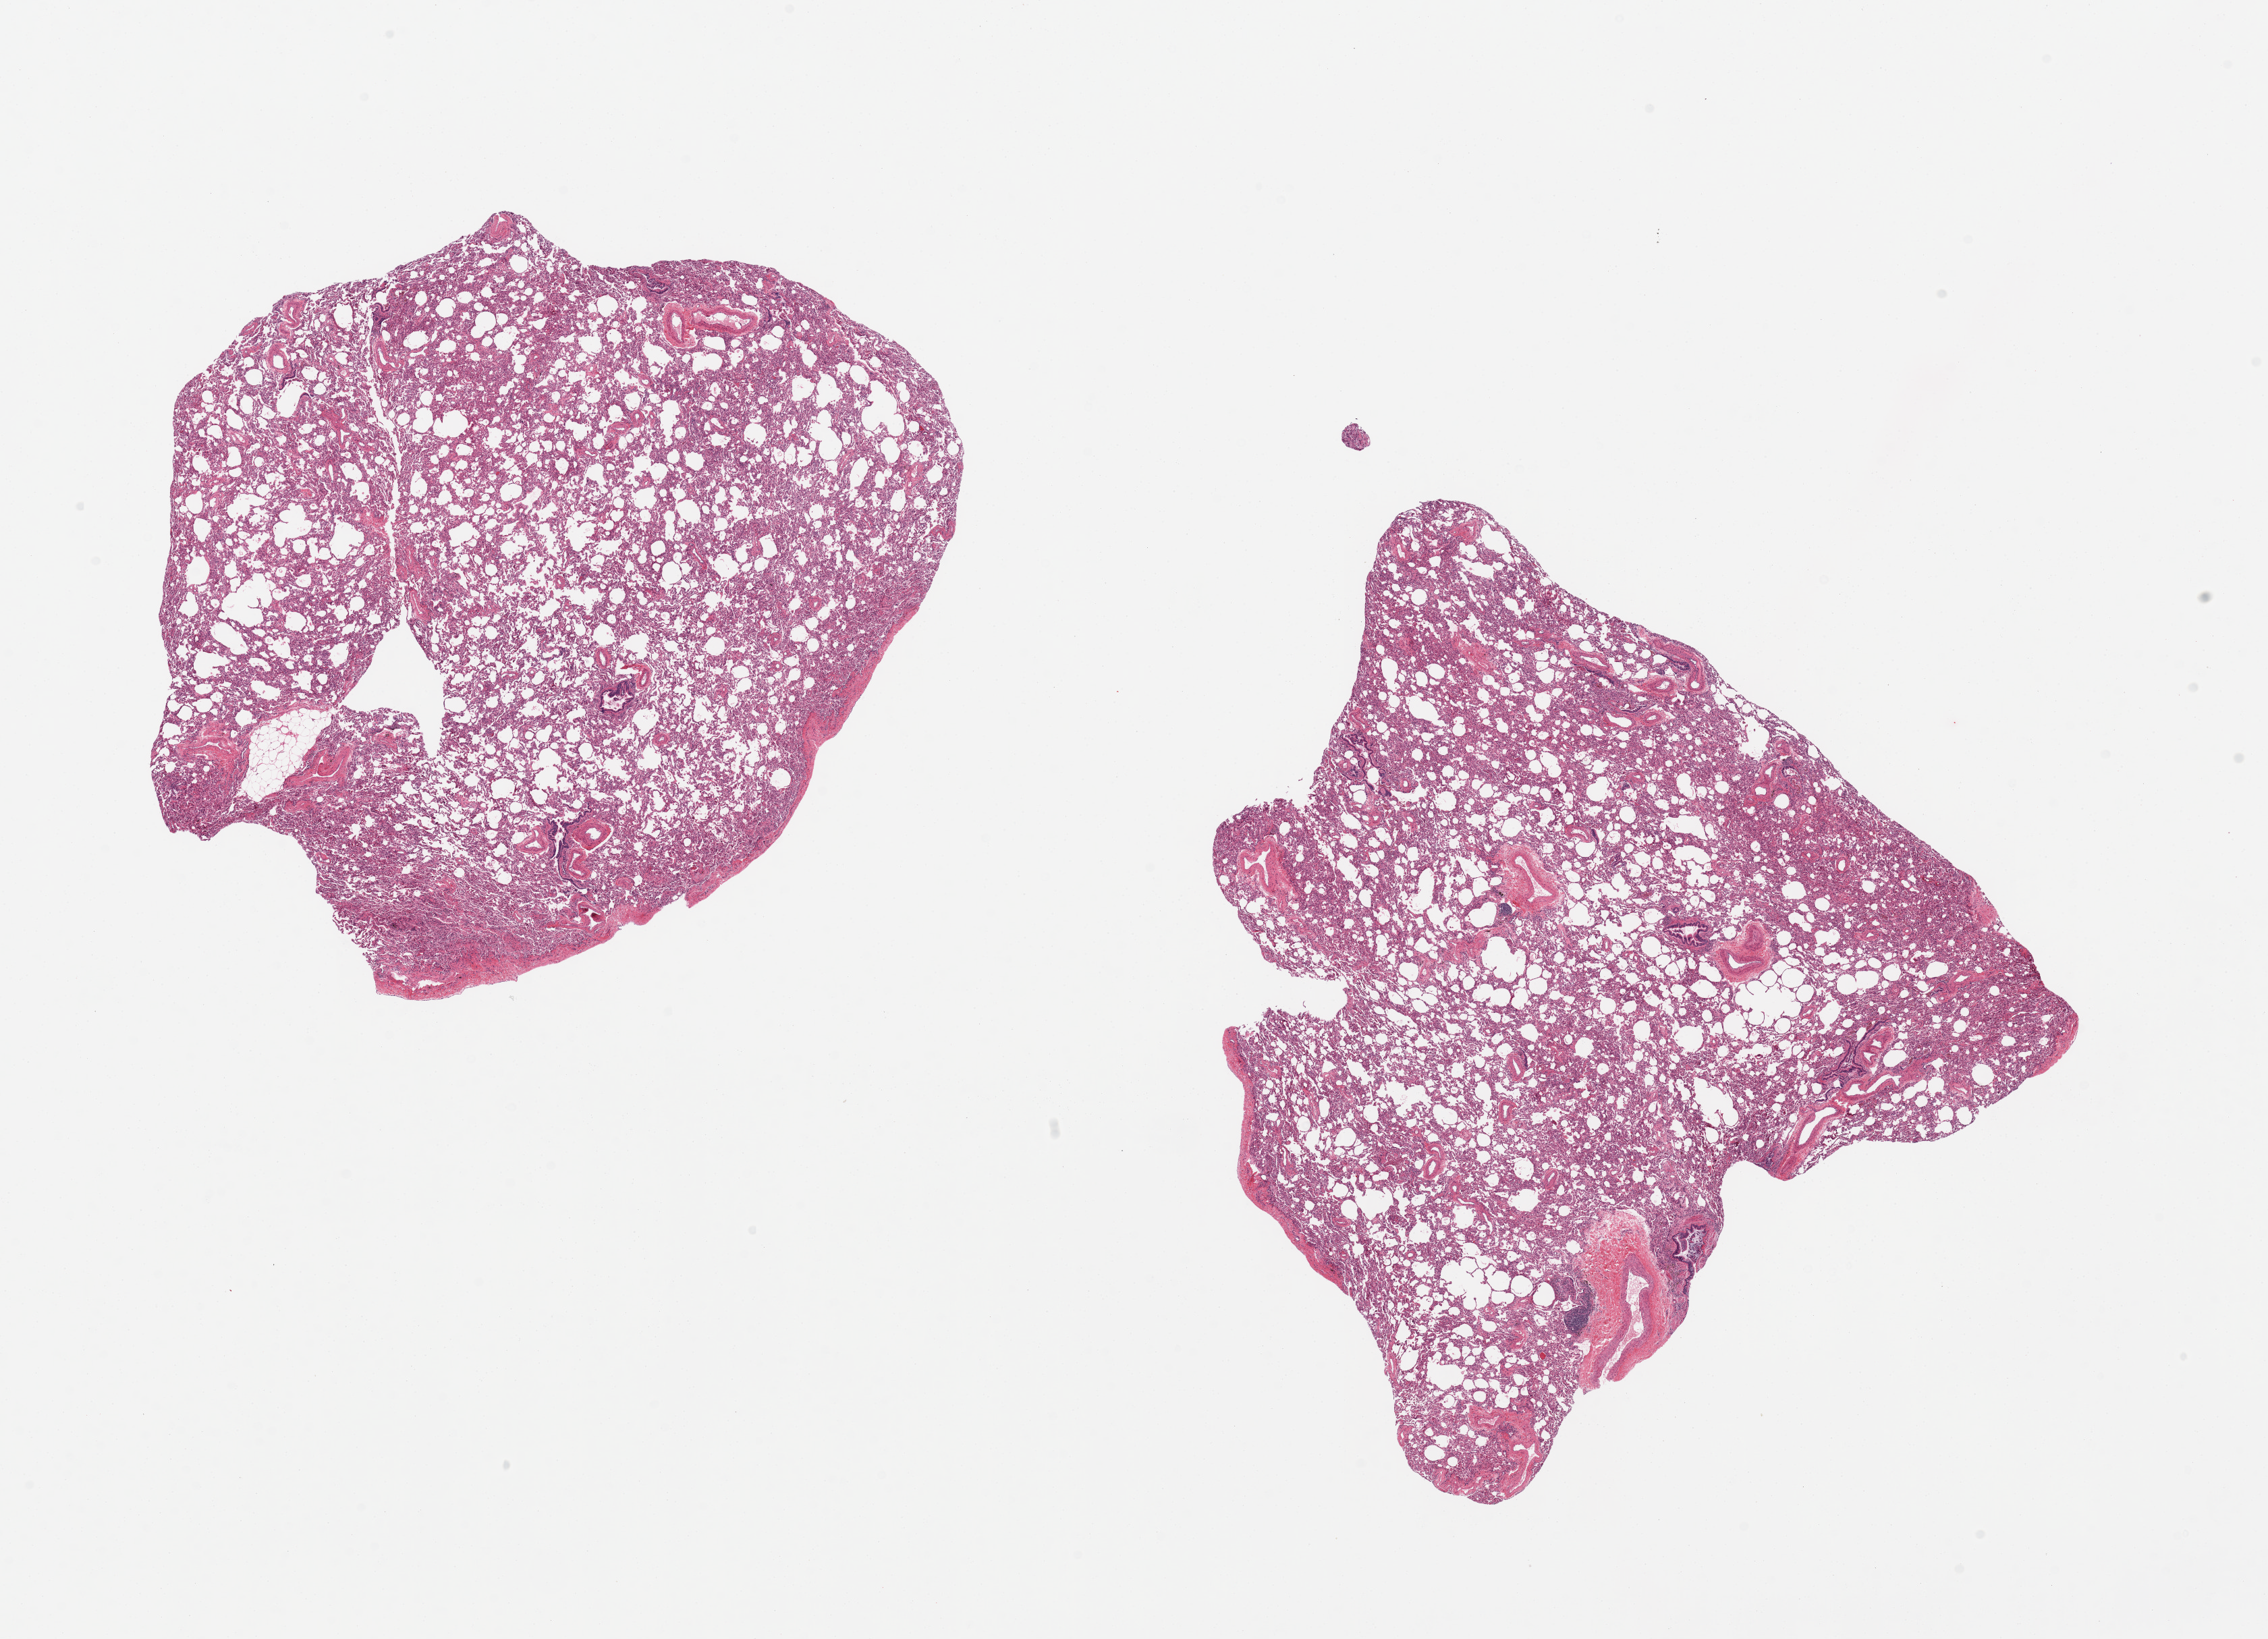
H&E whole-slide image, a low-resolution overview of the entire scanned area, about 26.6 x 19.2 mm (from a 20x scan). PAXgene-fixed paraffin-embedded (PFPE) section. Section of lung (target tissue). Tissue donor sample. Donor sex: male.
- pathologist's review note for this sample: 2 pieces, minimal congestion